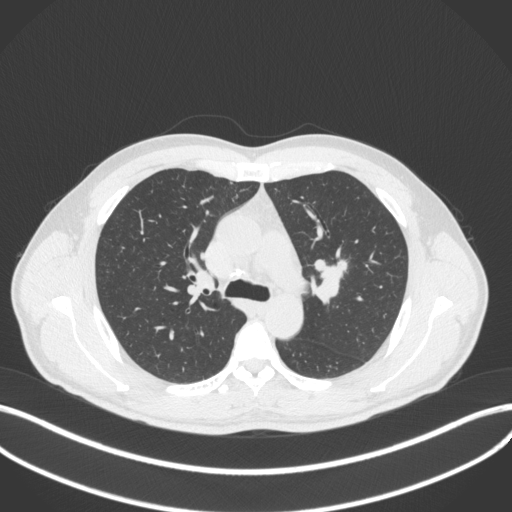
Chest CT, one axial slice. Position 280 of 383 along the scan axis. Lung window (W 1500 / L -600 HU). 1 mm slice thickness. 512 × 512 image matrix, field of view 400 × 400 mm. Male patient, age 50 years. From the clinical record (not read from this slice): clinical TNM (as recorded): T1c N1 M1b.
Outlined on this slice (bounding box drawn by a radiologist):
- lung tumour (recorded histology: squamous cell carcinoma): bounding box <309,250,349,310> (left, top, right, bottom; pixels)